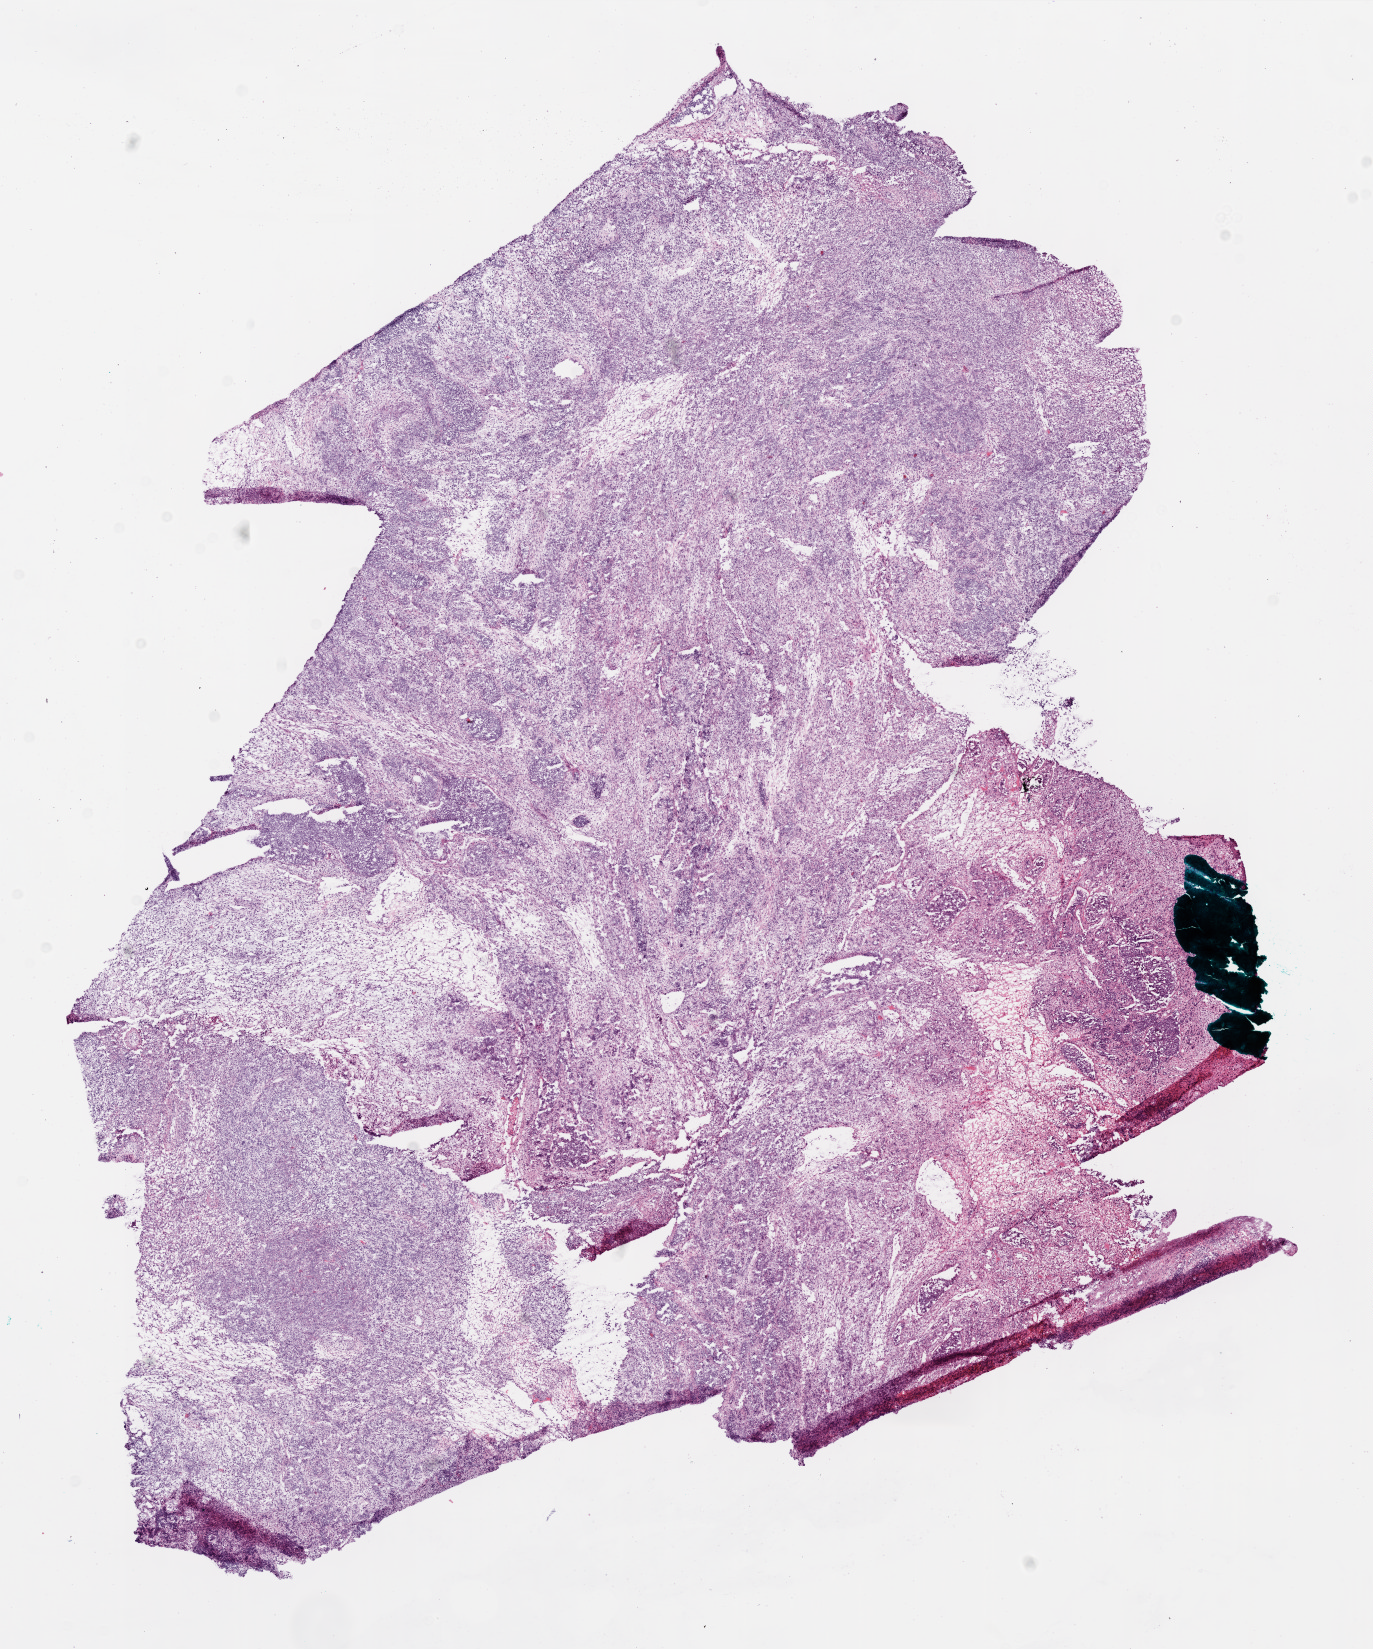
H&E-stained whole-slide image — shown as a low-resolution overview of the whole scanned area (about 11.0 x 13.2 mm, acquisition: 20x scan); frozen section from the bottom of the tissue portion; brain, primary tumour sample. Patient: male, age at initial diagnosis 42 years. Pathologist review of this section (percent, as recorded): tumour cells 80%, tumour nuclei 85%, stromal cells 15%, necrosis 5%.
Histologic diagnosis: Glioblastoma.